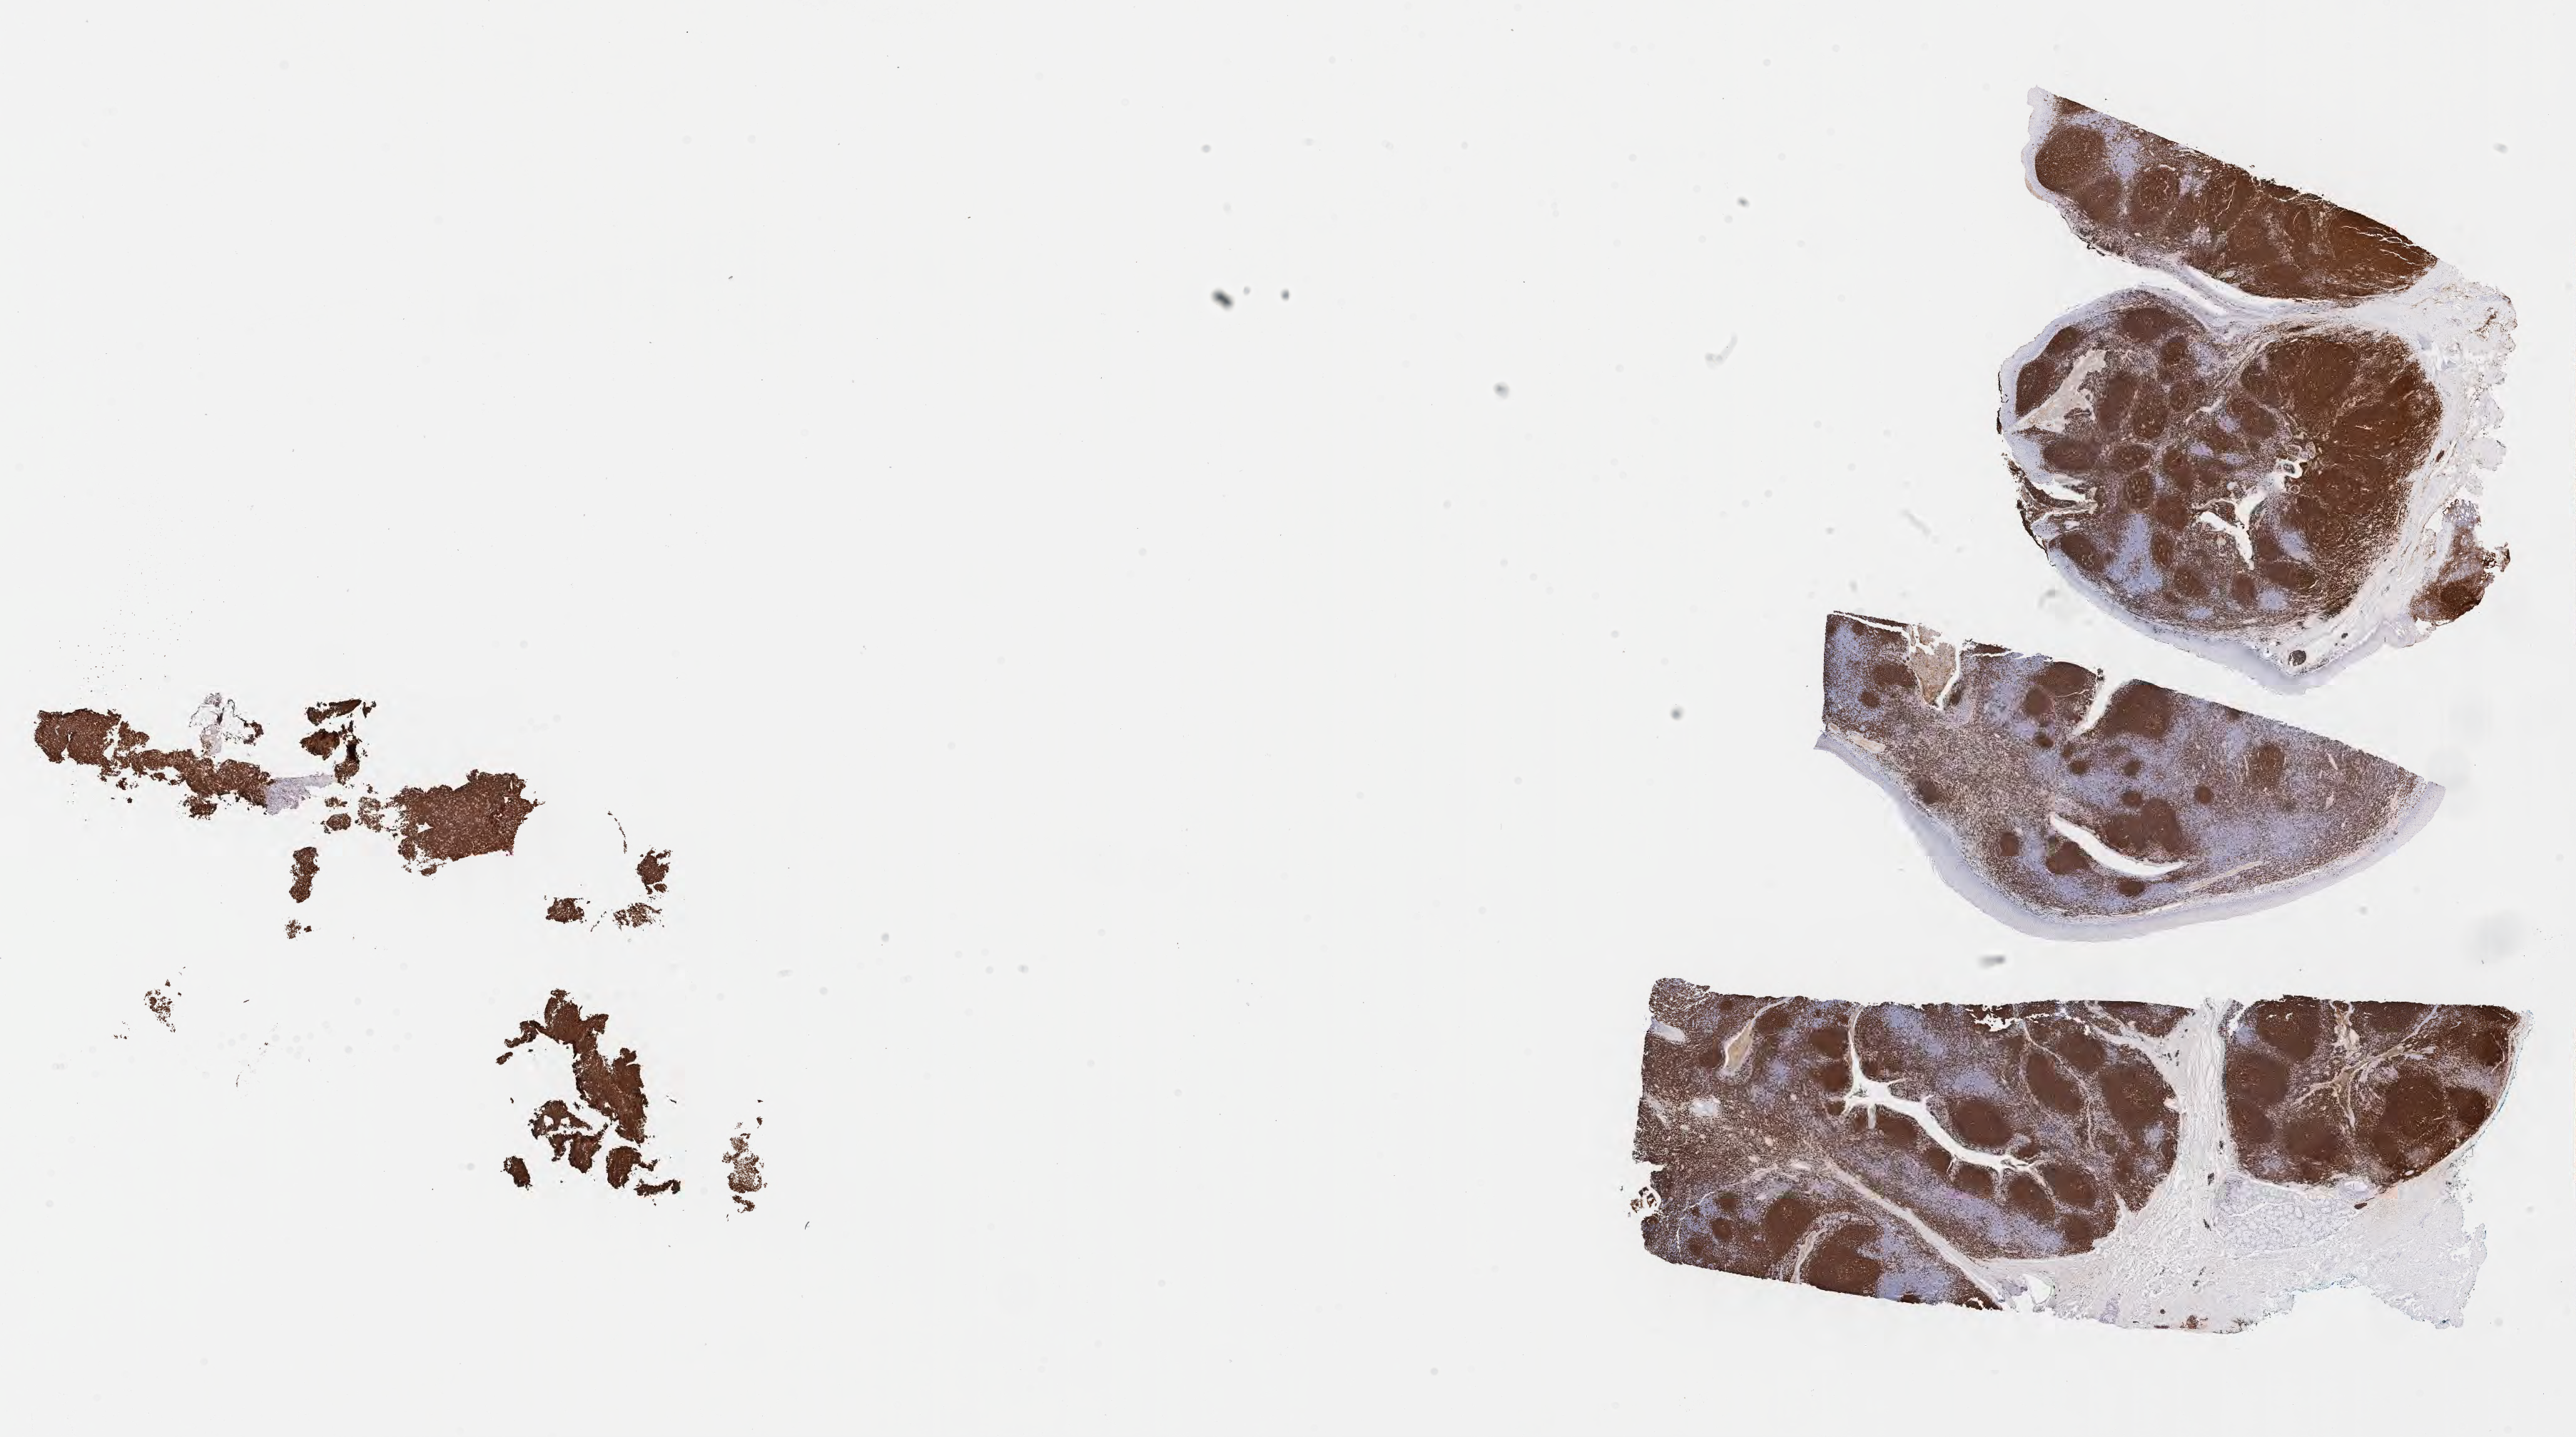
Immunohistochemistry (IHC) whole-slide image stained for CD20, low-resolution overview of the scanned area, about 29.2 x 16.3 mm, specimen: tumor tissue, site: cranium. Female patient; age at initial diagnosis 1 years.
• histologic diagnosis: Burkitt lymphoma, NOS